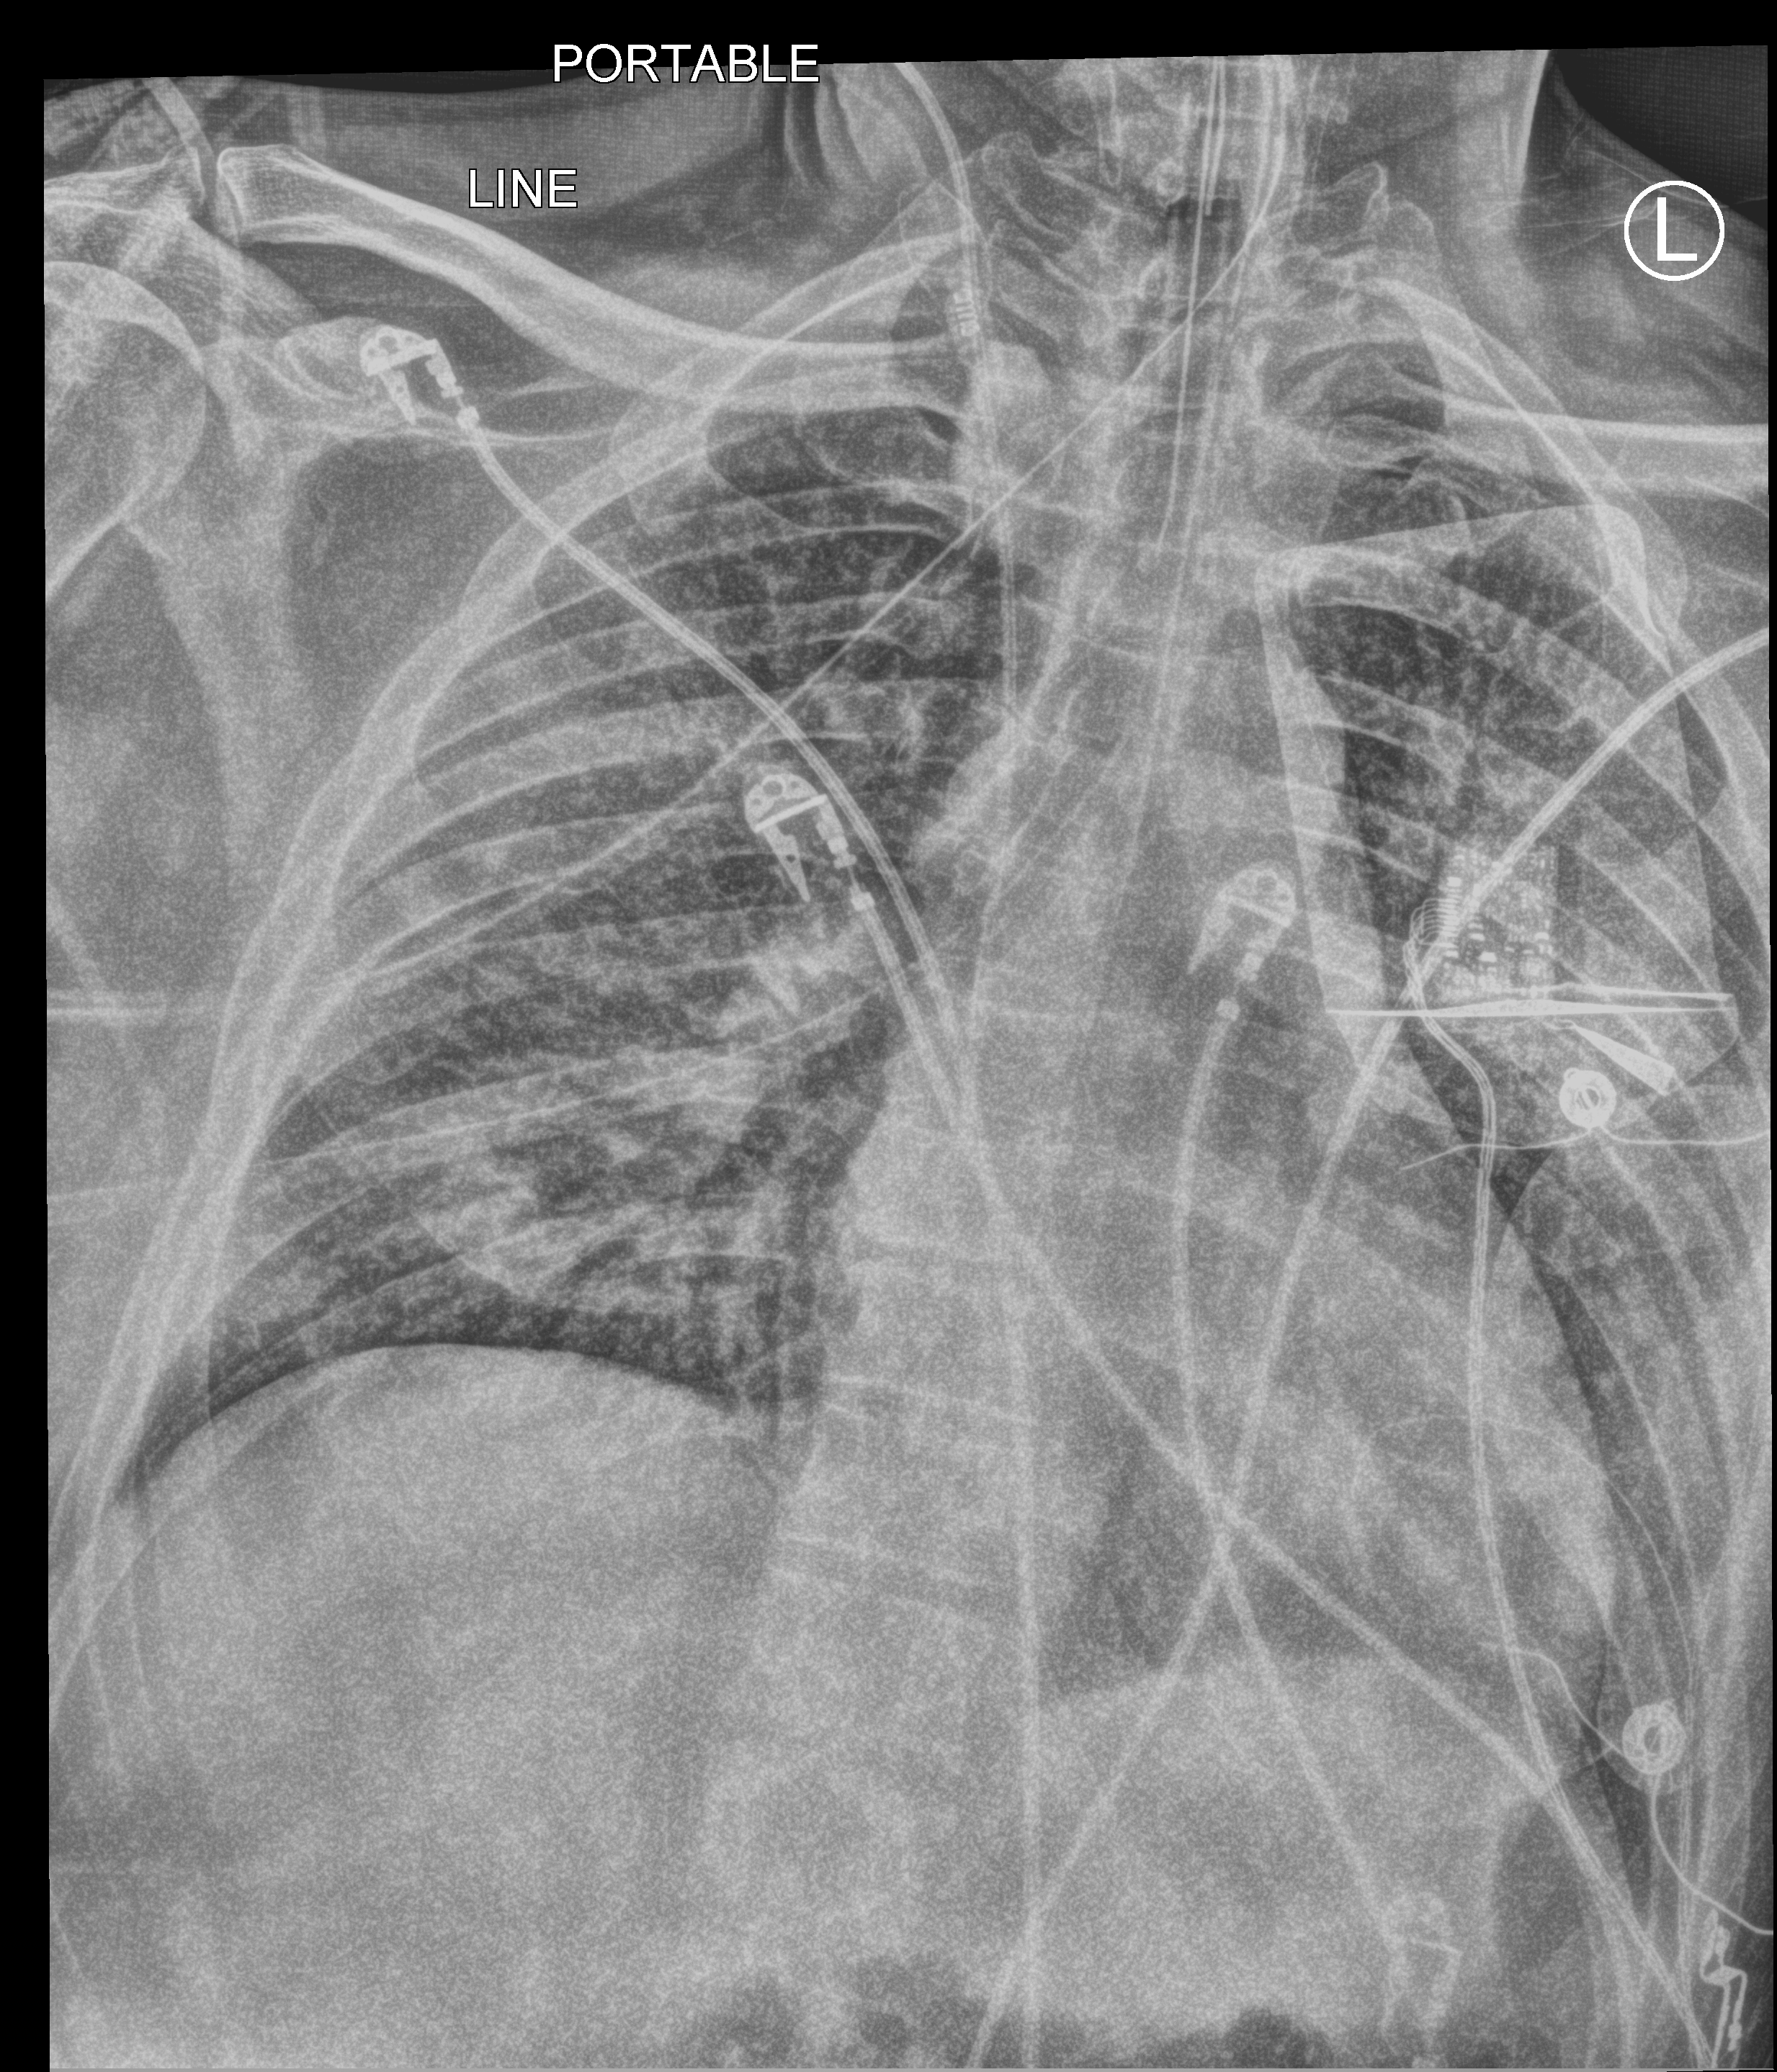
Bedside chest radiograph (computed radiography); anteroposterior (AP) projection. Male patient hospitalised with COVID-19, age 18–59 years.
Admission-level facts for this patient (not findings on this image; timing relative to this image not recorded): mechanically ventilated during this hospital stay: yes; diabetes (admission record): no.